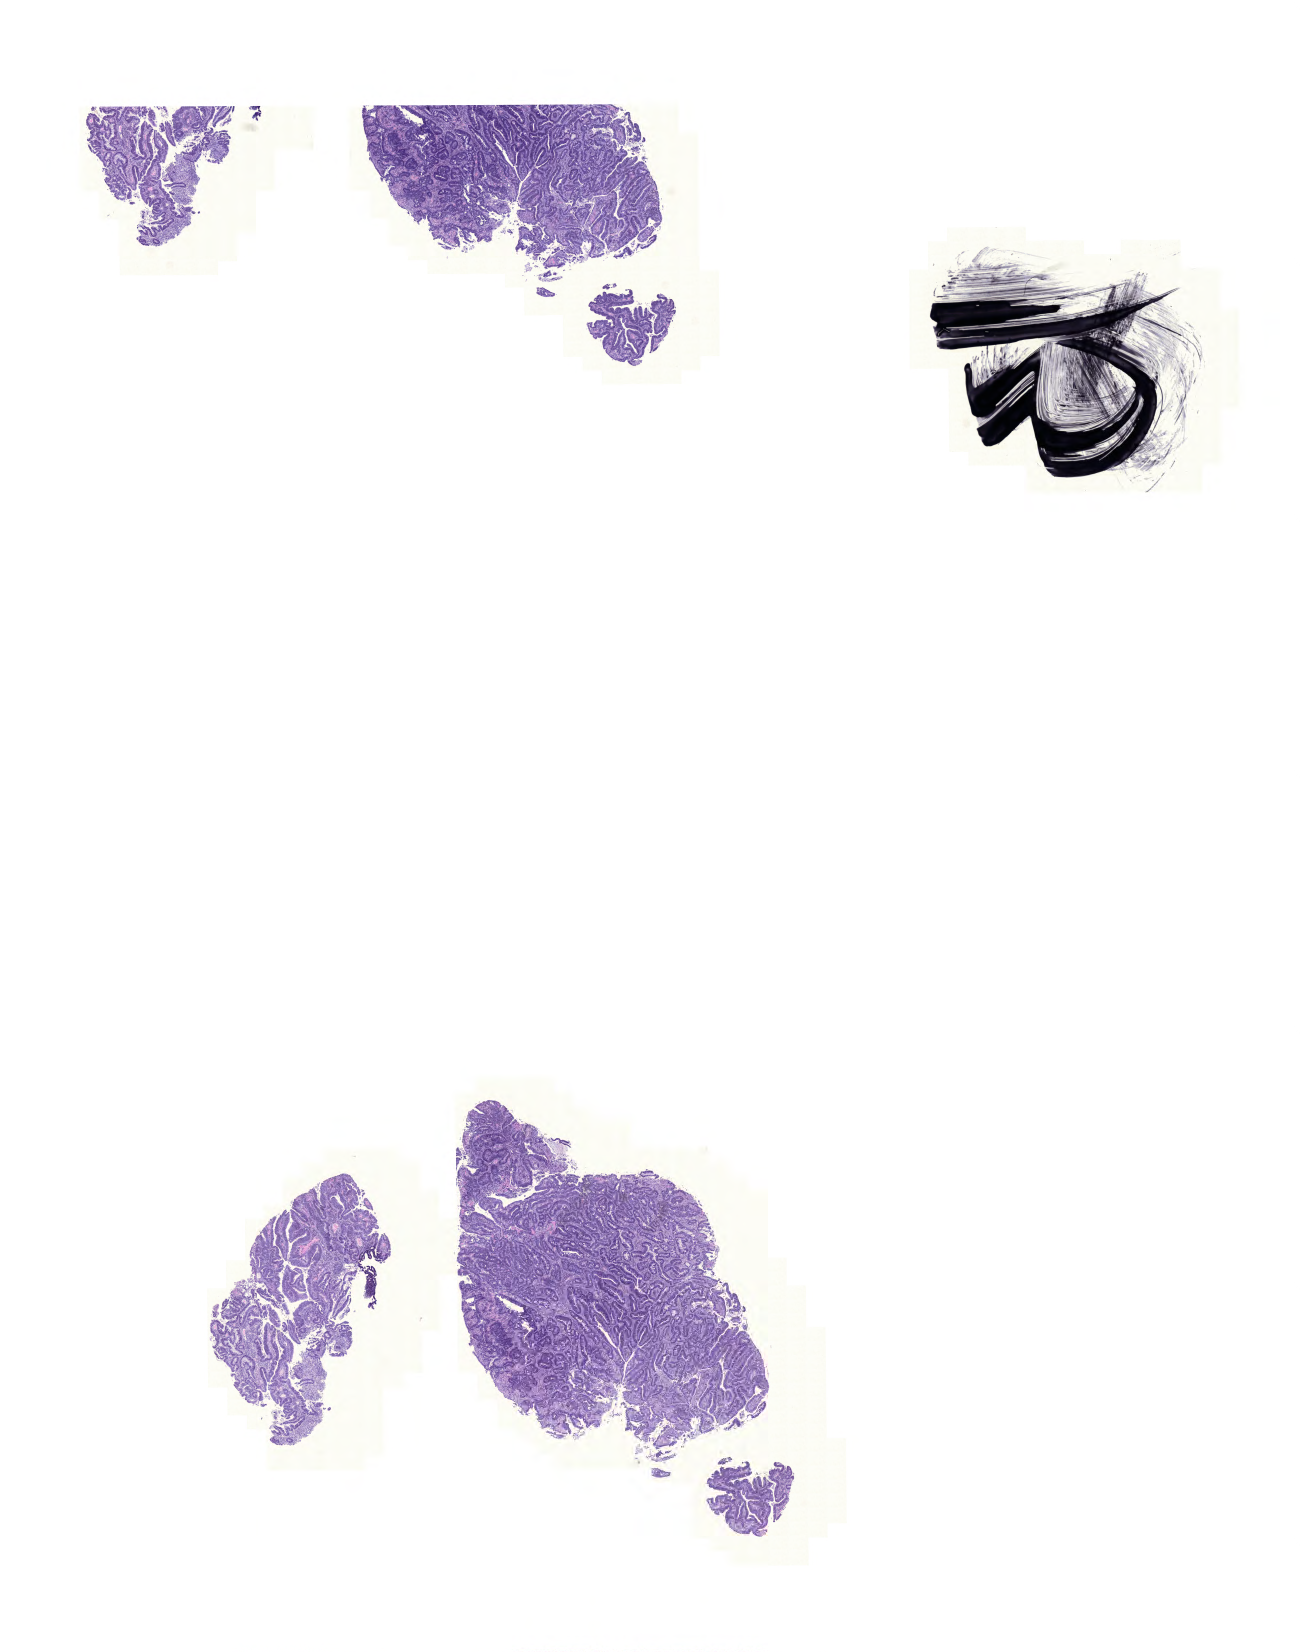
H&E whole-slide image, whole scanned area (about 19.3 x 24.6 mm, from a 20x scan) shown as a low-resolution overview. Formalin-fixed paraffin-embedded (FFPE) diagnostic section. Sample: primary tumour, rectum. Patient: male, age at initial diagnosis 62 years.
AJCC pathologic stage: I (6th edition). Diagnosis: Adenocarcinoma, NOS.